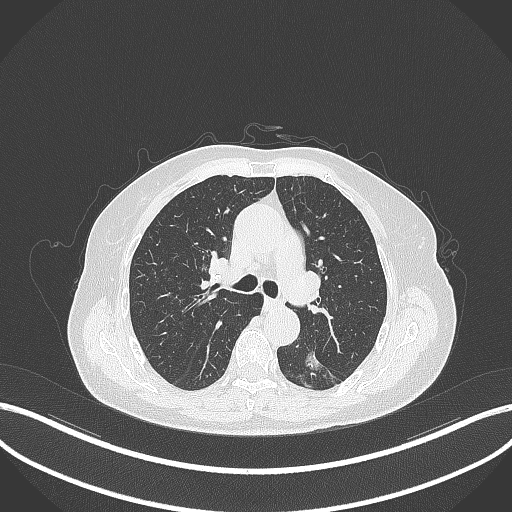
Chest CT, one axial slice; slice 195 of 352 in the series (ordered by position); lung window (W 1500 / L -600 HU); 1 mm slice thickness; 512 × 512 image matrix, field of view 400 × 400 mm. Female patient, age 70 years. Case-level facts recorded for this patient, not image findings: clinical TNM (as recorded): T1c N0 M0.
Structures marked on this image (bounding box drawn by a radiologist):
- lung tumour (recorded histology: adenocarcinoma): bounding box <298,342,325,380> (left, top, right, bottom; pixels)